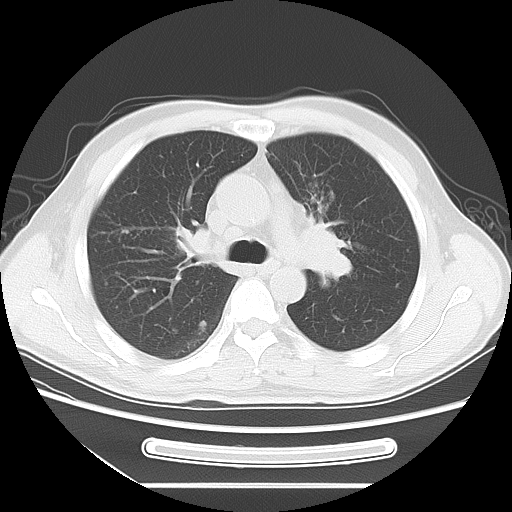
Chest CT, one axial slice. 120 kVp. Lung window (W 1500 / L -600 HU). 5 mm slice thickness. 512 × 512 image matrix, field of view 366 × 366 mm. Patient: male, 51 years. From the clinical record (not read from this slice): clinical TNM (as recorded): T1c N3 M0.
Annotated regions visible in this slice (bounding box drawn by a radiologist):
- lung tumour (recorded histology: adenocarcinoma): bounding box <293,210,362,300> (left, top, right, bottom; pixels)